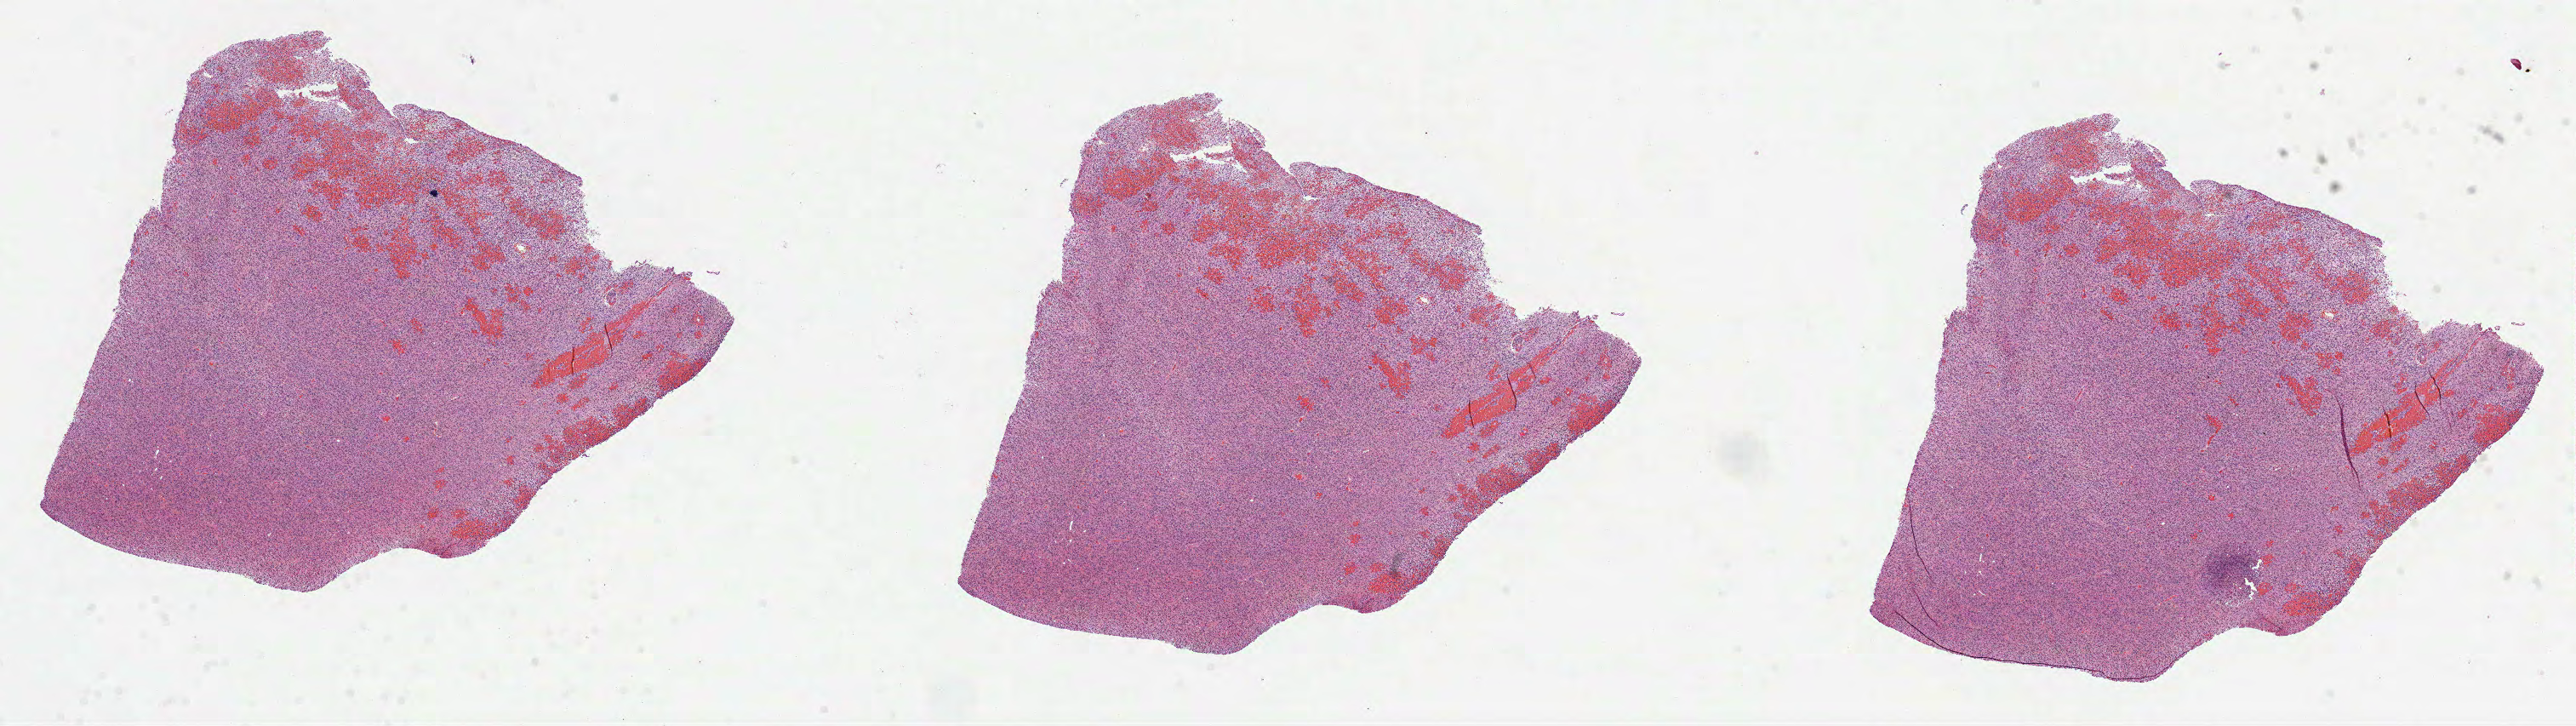
Hematoxylin and eosin (H&E) stained whole-slide image, low-resolution overview of the scanned area, about 24.4 x 6.9 mm; formalin-fixed paraffin-embedded (FFPE) diagnostic section; primary tumour sample from the brain. Patient: male, age at initial diagnosis 63 years.
Pathologic diagnosis: Glioblastoma.